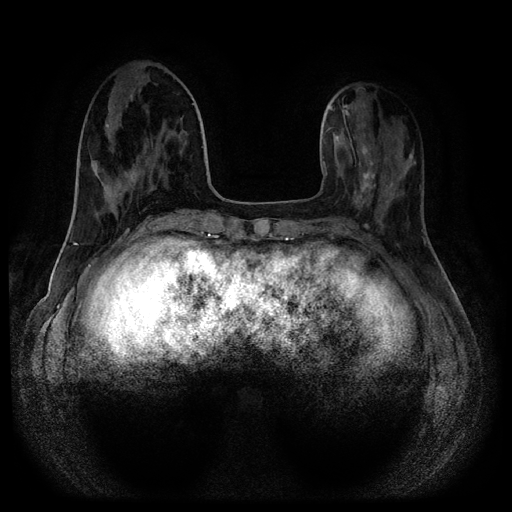
Breast MRI (dynamic contrast-enhanced, multi-phase), one axial slice; dynamic contrast-enhanced series, time point 2 of 5 at this slice position (early post-contrast); 1.5 T; TE 2.7 ms, TR 5.4 ms; 2 mm slice thickness; 512 × 512 image matrix. Patient: female, 40 years.
Annotated regions visible in this slice (semi-automatically segmented with operator editing):
- breast lesion (labelled benign in the annotation): bounding box <351,144,382,211> (left, top, right, bottom; pixels)